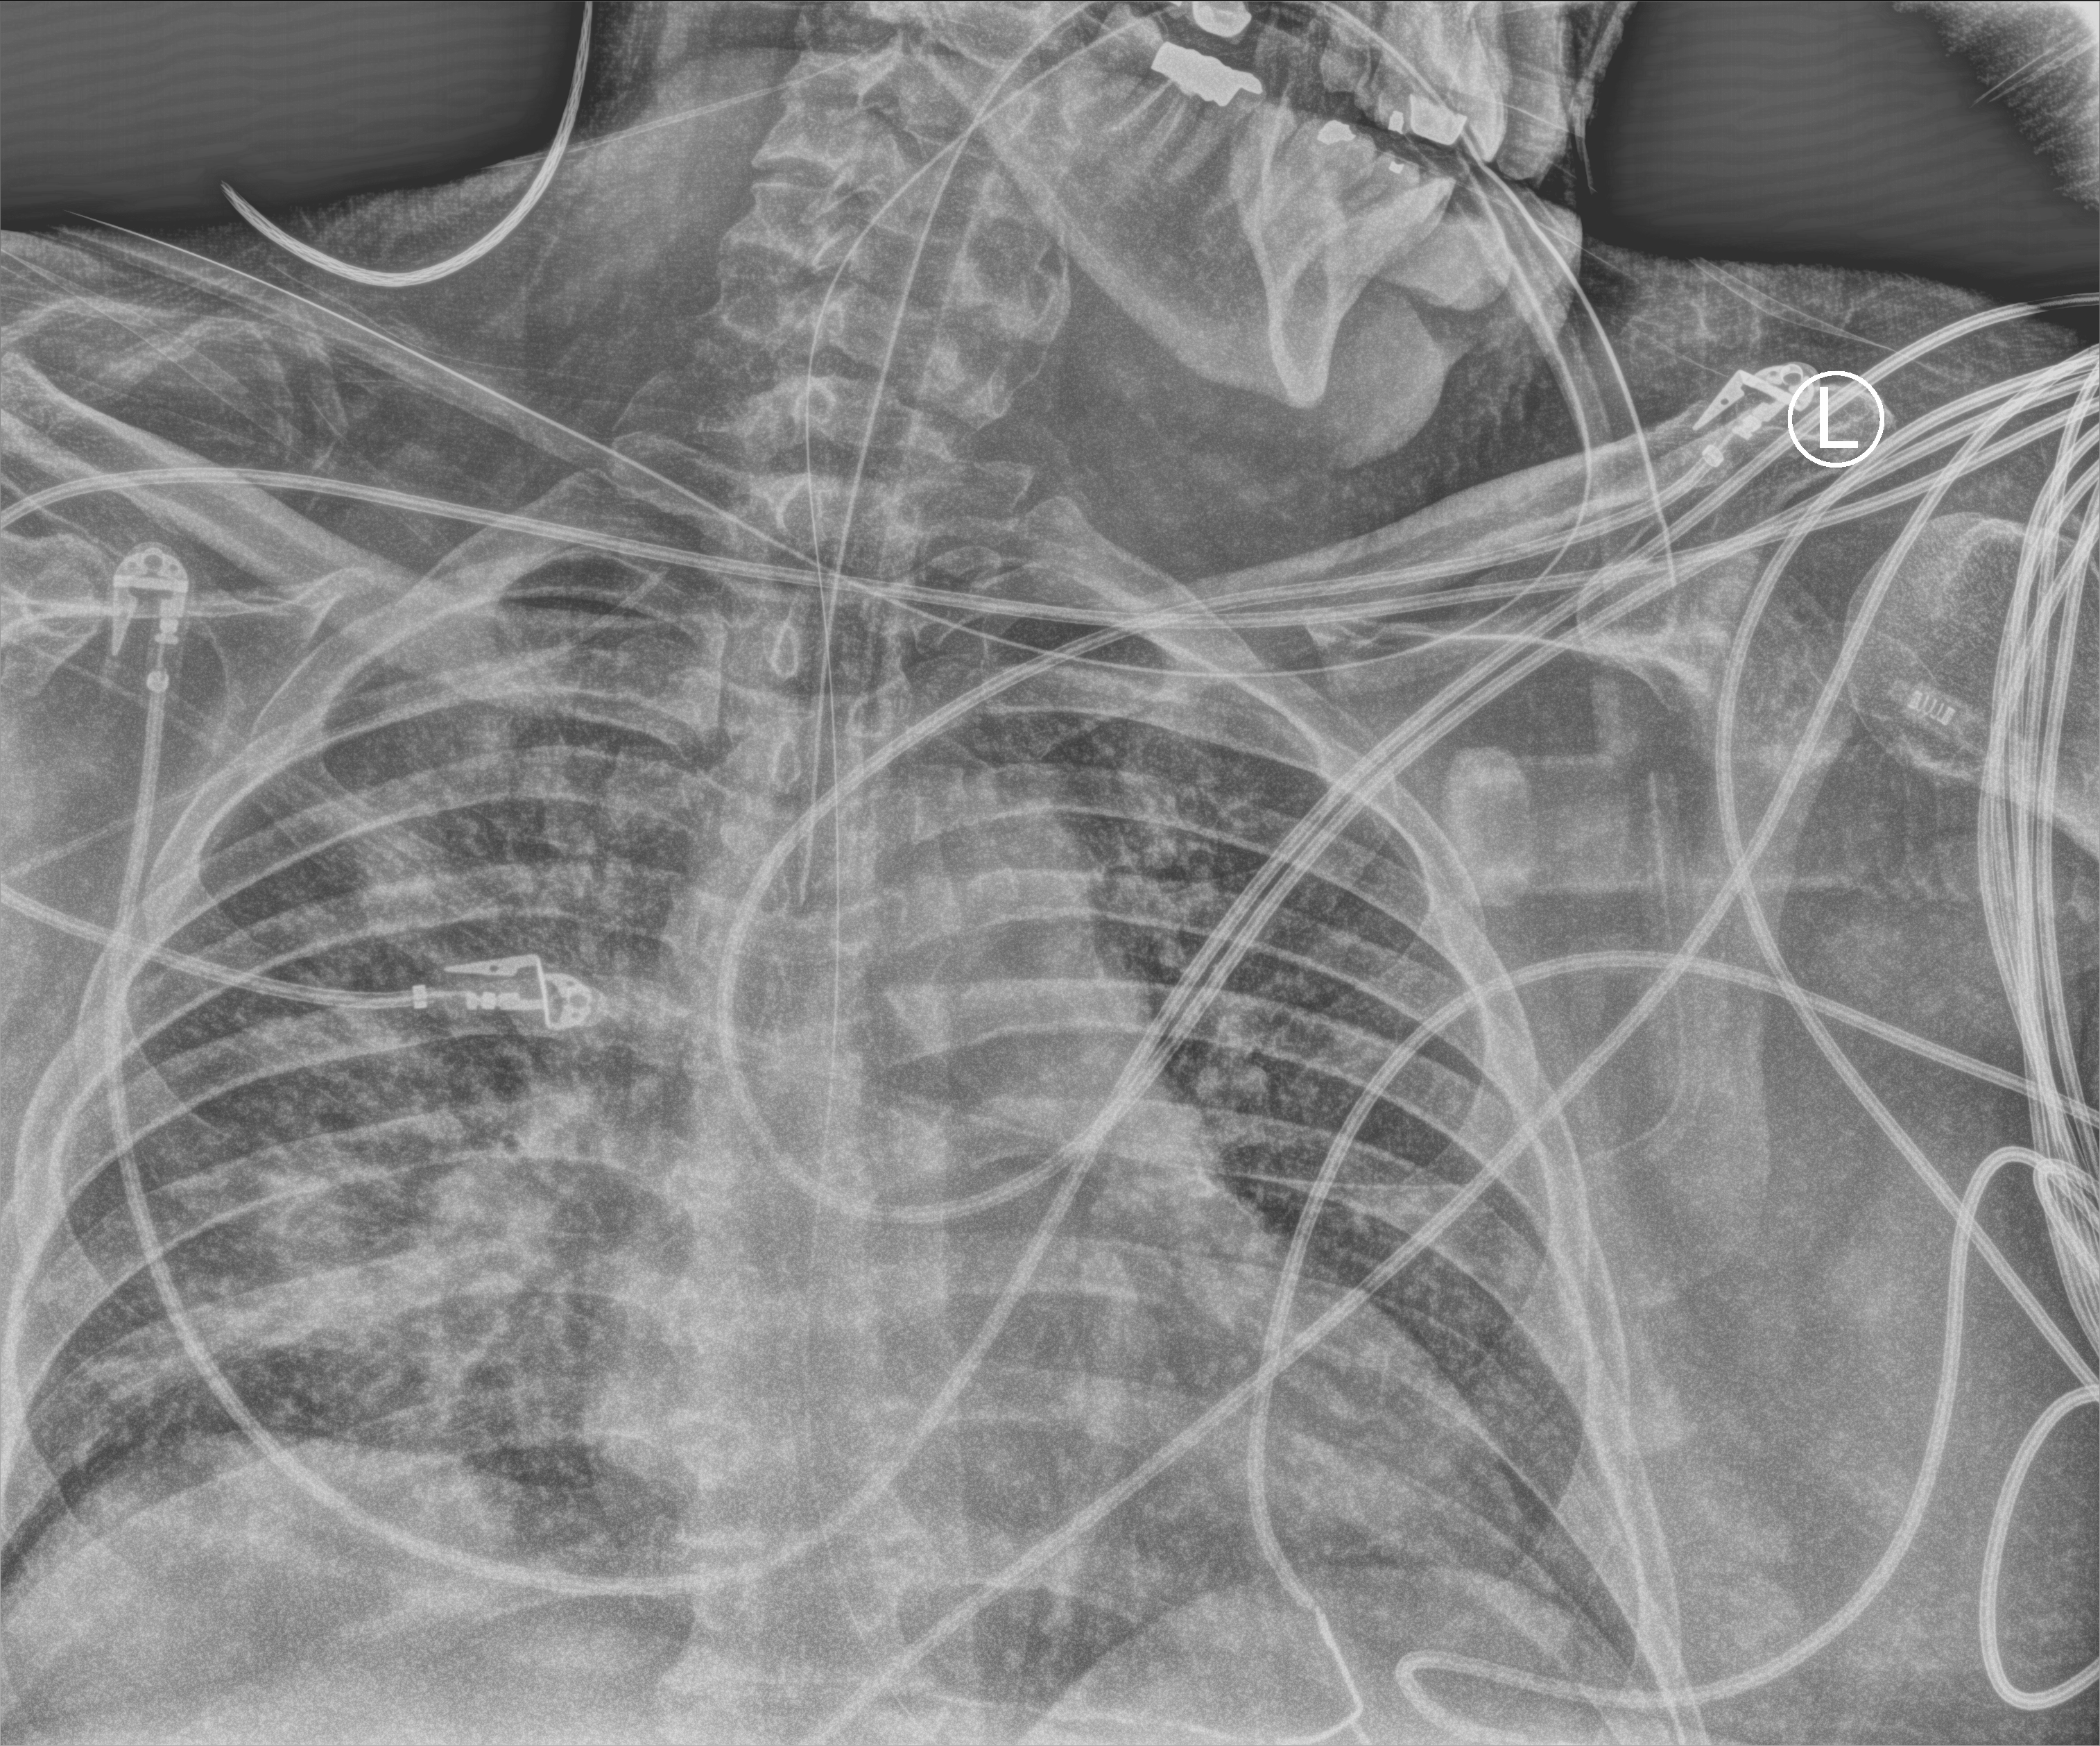
Chest X-ray (portable). Male patient hospitalised with COVID-19, age 18–59 years.
Hospital-stay facts (about this admission, not read from this image; timing relative to this image not recorded): mechanically ventilated during this hospital stay: yes; admitted to intensive care during this hospital stay: yes.